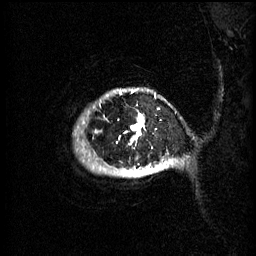
Breast MRI (dynamic contrast-enhanced), one sagittal slice. Slice 57 of 60 in the series (ordered by position). 3 images stored at this slice position (order not interpretable as contrast timing). 1.5 T. TE 4.2 ms, TR 11 ms. 256 × 256 image matrix, field of view 220 × 220 mm. Patient: female, 51 years.
Outlined on this slice (semi-automatic segmentation, software-assisted and operator-edited):
- analysis volume of interest (the breast-tissue region the enhancement analysis was run in; not a lesion): bounding box [x1, y1, x2, y2] px = [83, 90, 176, 177]
- tumour enhancement mask (voxels above the 70 % enhancement threshold inside the analysis volume of interest): [125, 90, 173, 175]